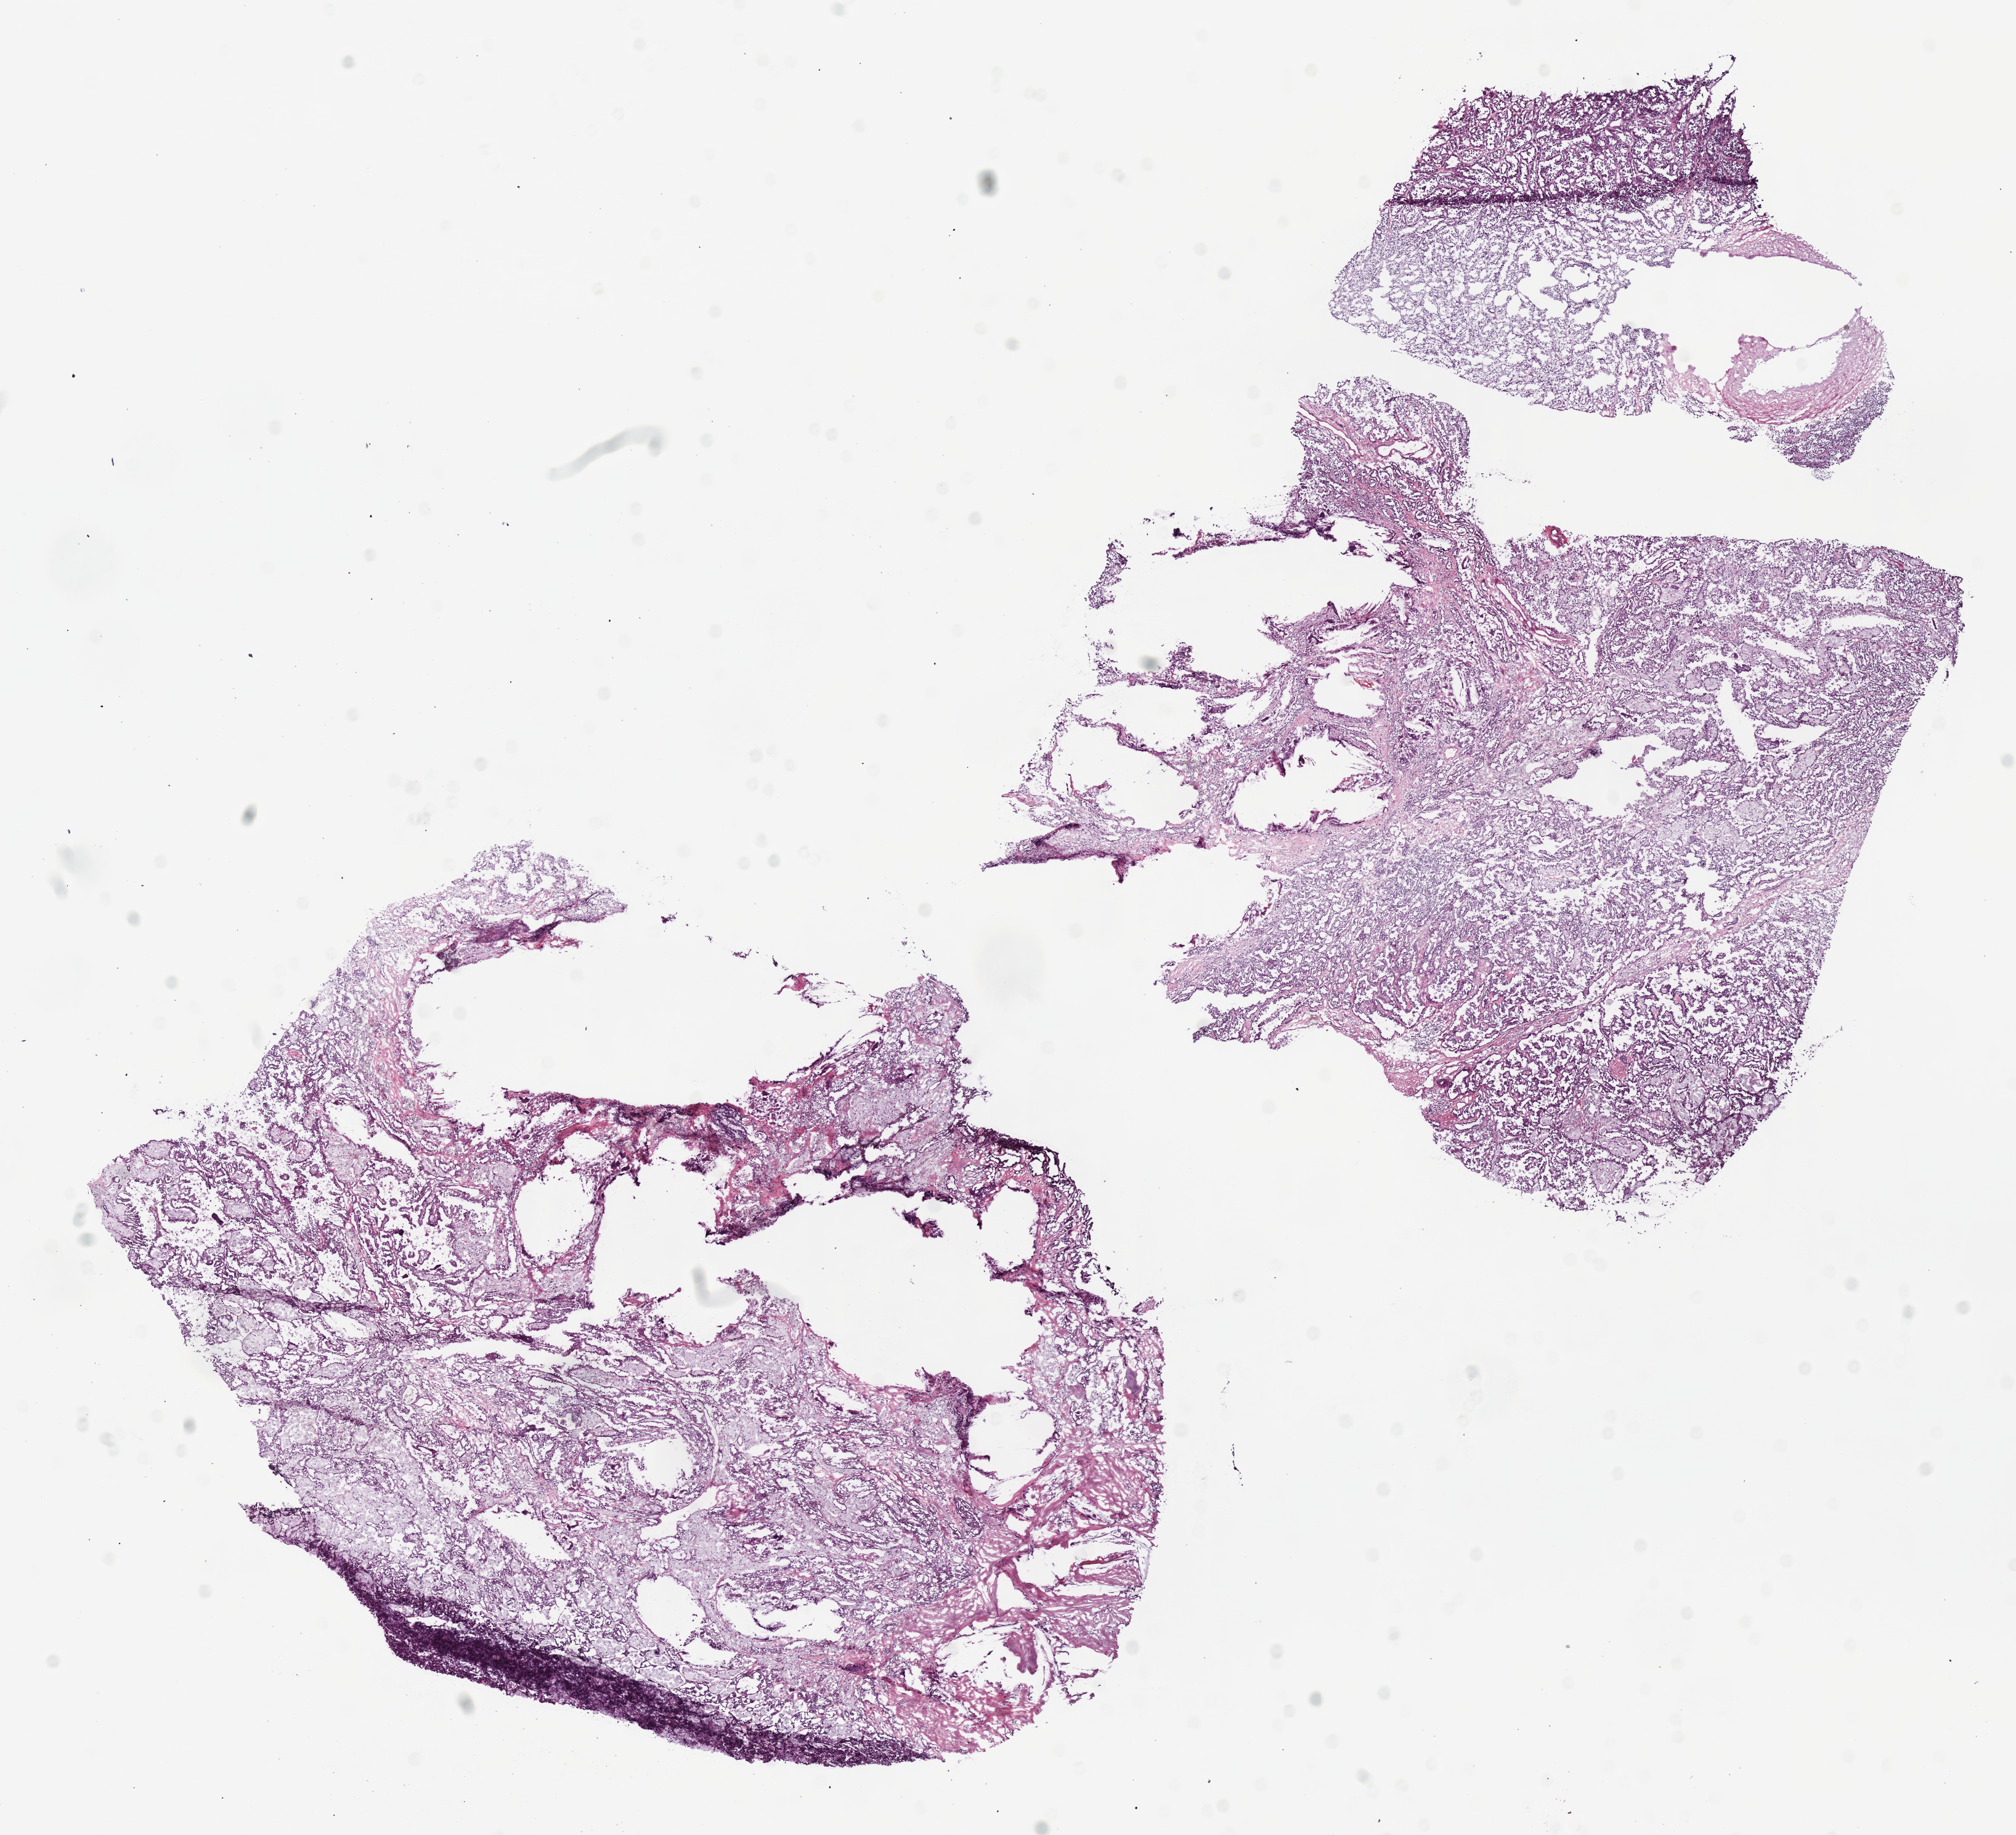
Whole-slide histology image, H&E — shown as a low-resolution overview of the whole scanned area (about 12.9 x 11.7 mm, from a 40x scan). Frozen section. Kidney, primary tumour sample. Male patient; age at initial diagnosis 83 years. Slide review estimates, as recorded: tumour cells 100%, tumour nuclei 75%, normal cells 0%, stromal cells 0%, necrosis 0%. Inflammatory infiltration, as recorded: lymphocyte infiltration 0%, monocyte infiltration 20%, neutrophil infiltration 0%.
Laterality: left. Diagnosis: Papillary adenocarcinoma, NOS. AJCC pathologic stage: I (7th edition).